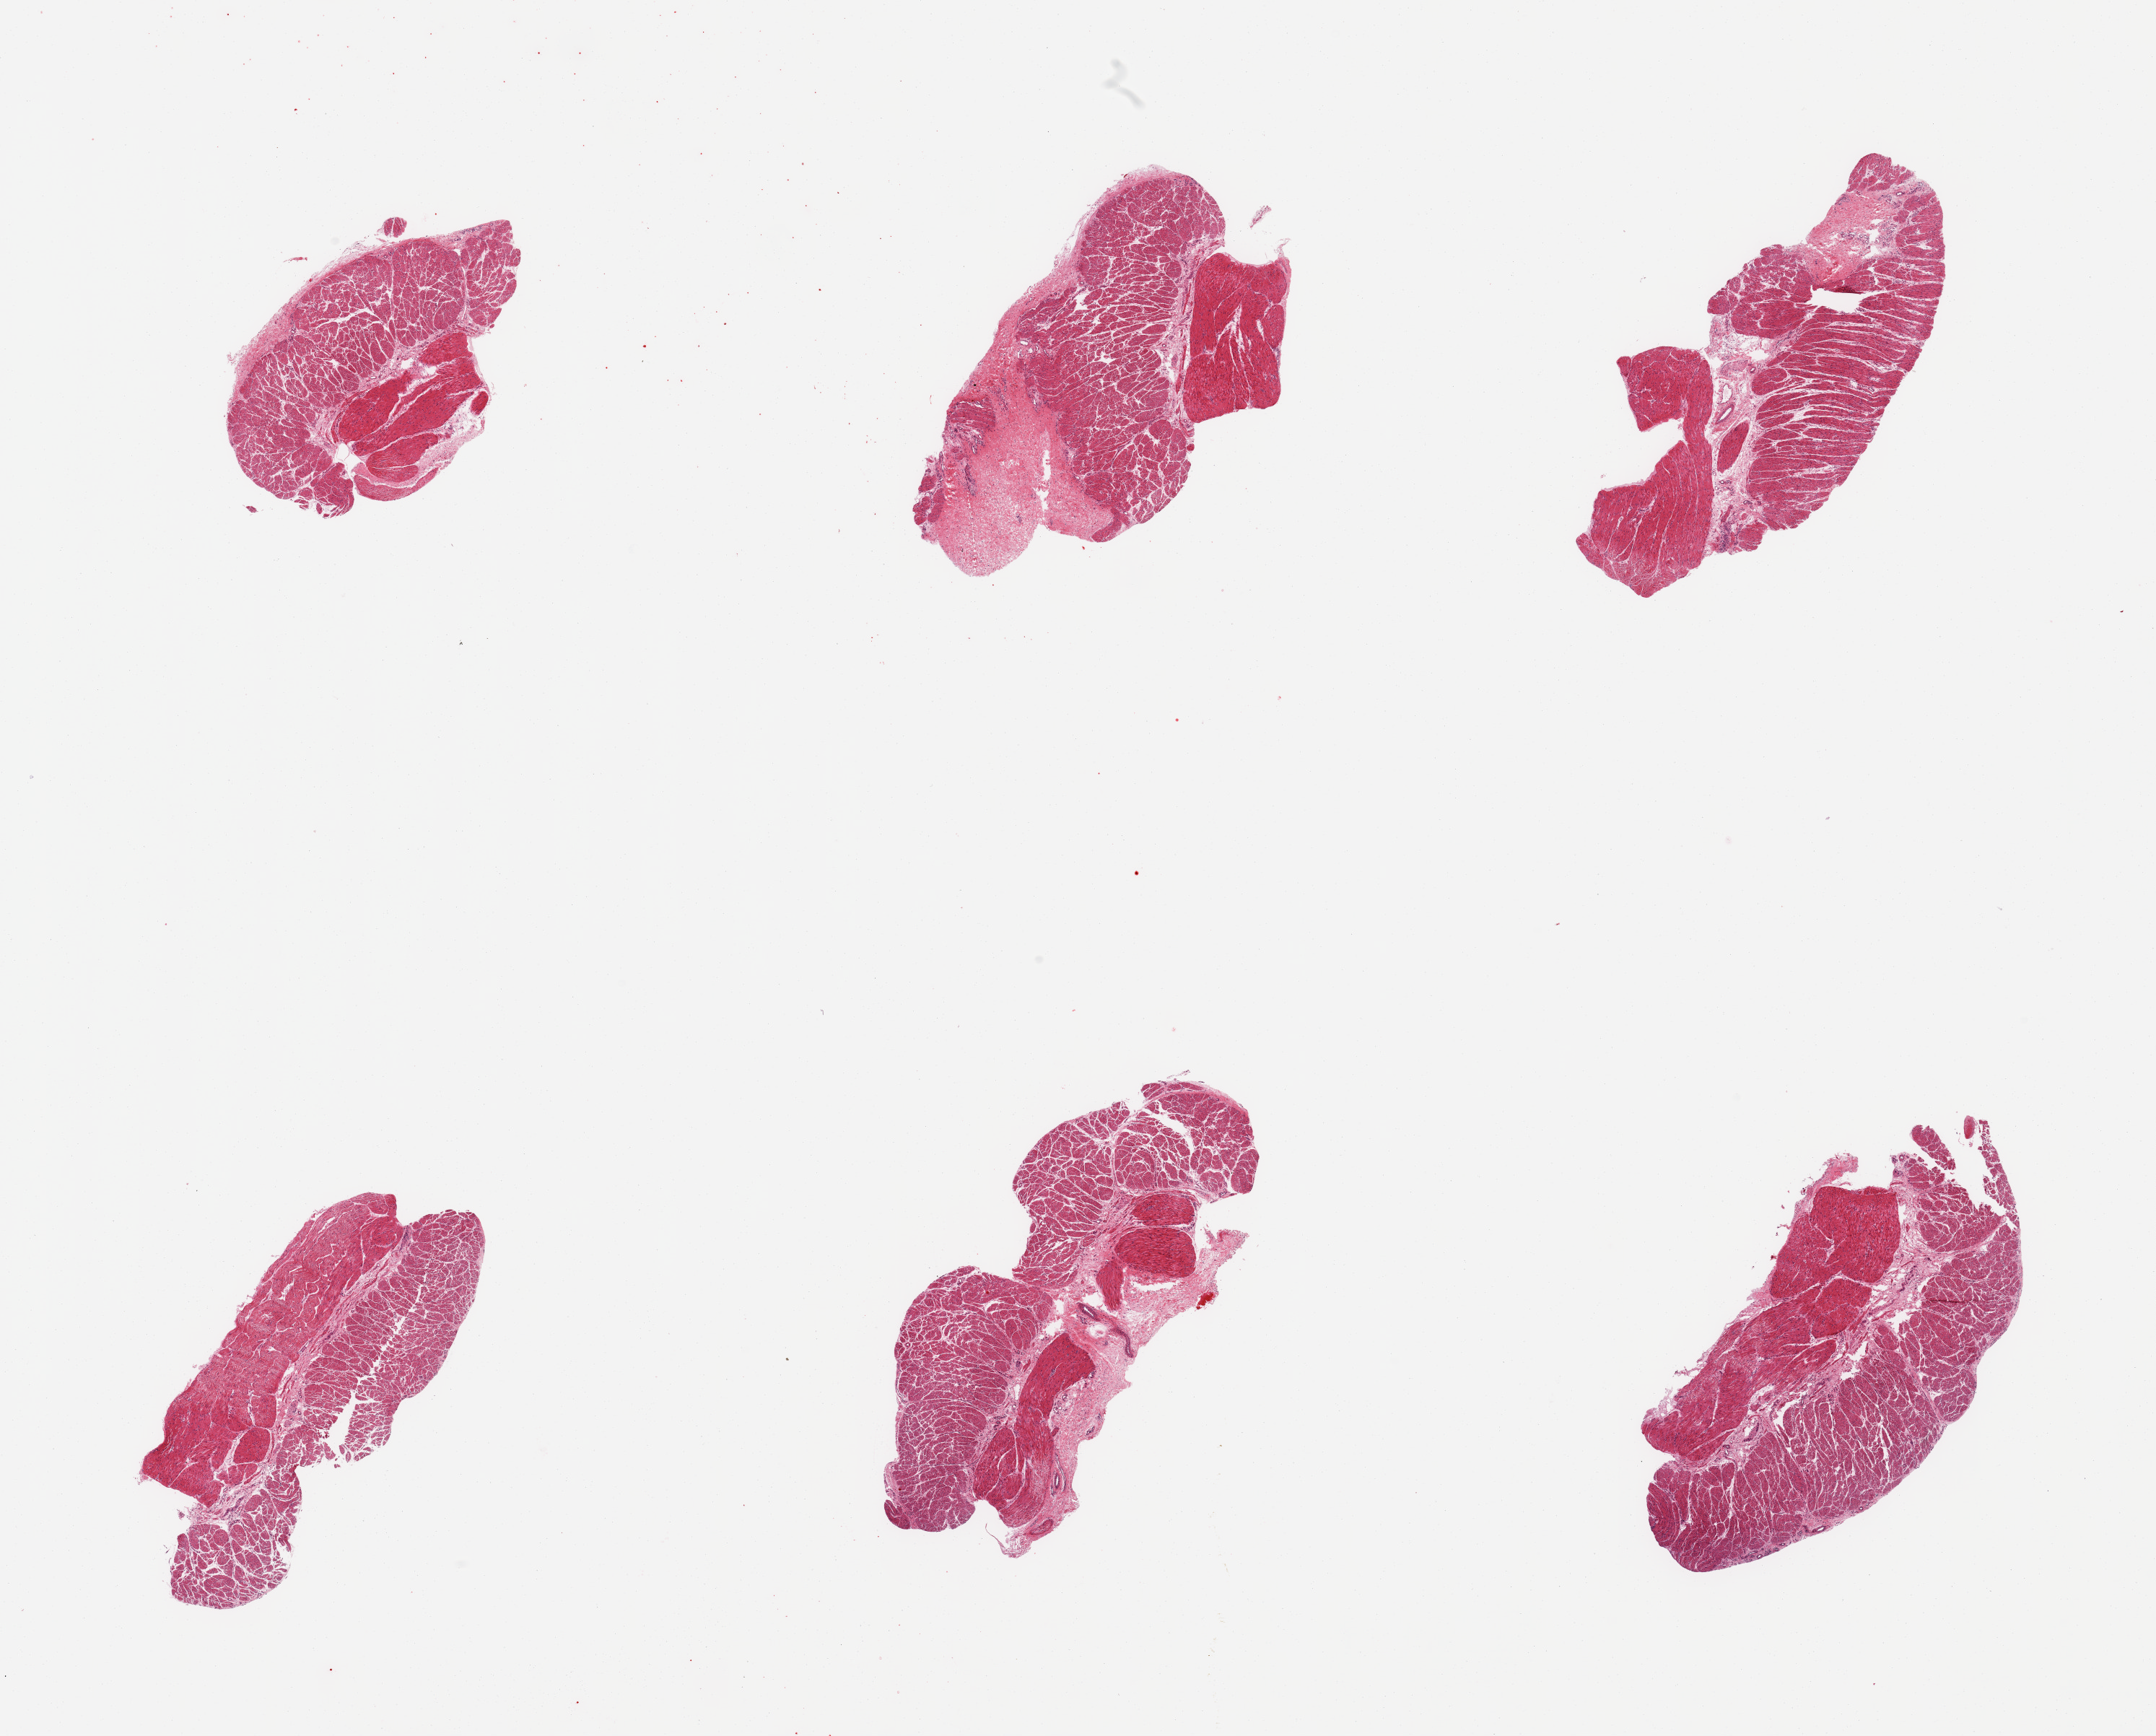
Digitized haematoxylin and eosin-stained section, low-resolution overview of the scanned area, about 23.6 x 19.0 mm (acquisition: 20x scan). PAXgene-fixed, paraffin-embedded tissue. Target tissue: esophageal muscle. Tissue donor sample. Male donor.
Review note (as recorded): 5 pieces, confirmed target muscularis.